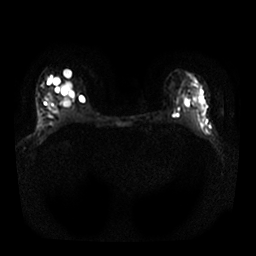
Breast MRI, one axial slice. Position 16 of 25 along the scan axis. Diffusion-weighted series; image 2 of 4 stored at this slice position (different b-values; order by instance number). 1.5 T. 256 × 256 image matrix. Female patient.
Structures marked on this image (manually delineated by an expert):
- tumour on diffusion-weighted imaging: bounding box (x1, y1, x2, y2) in pixels: (195, 88, 207, 121)